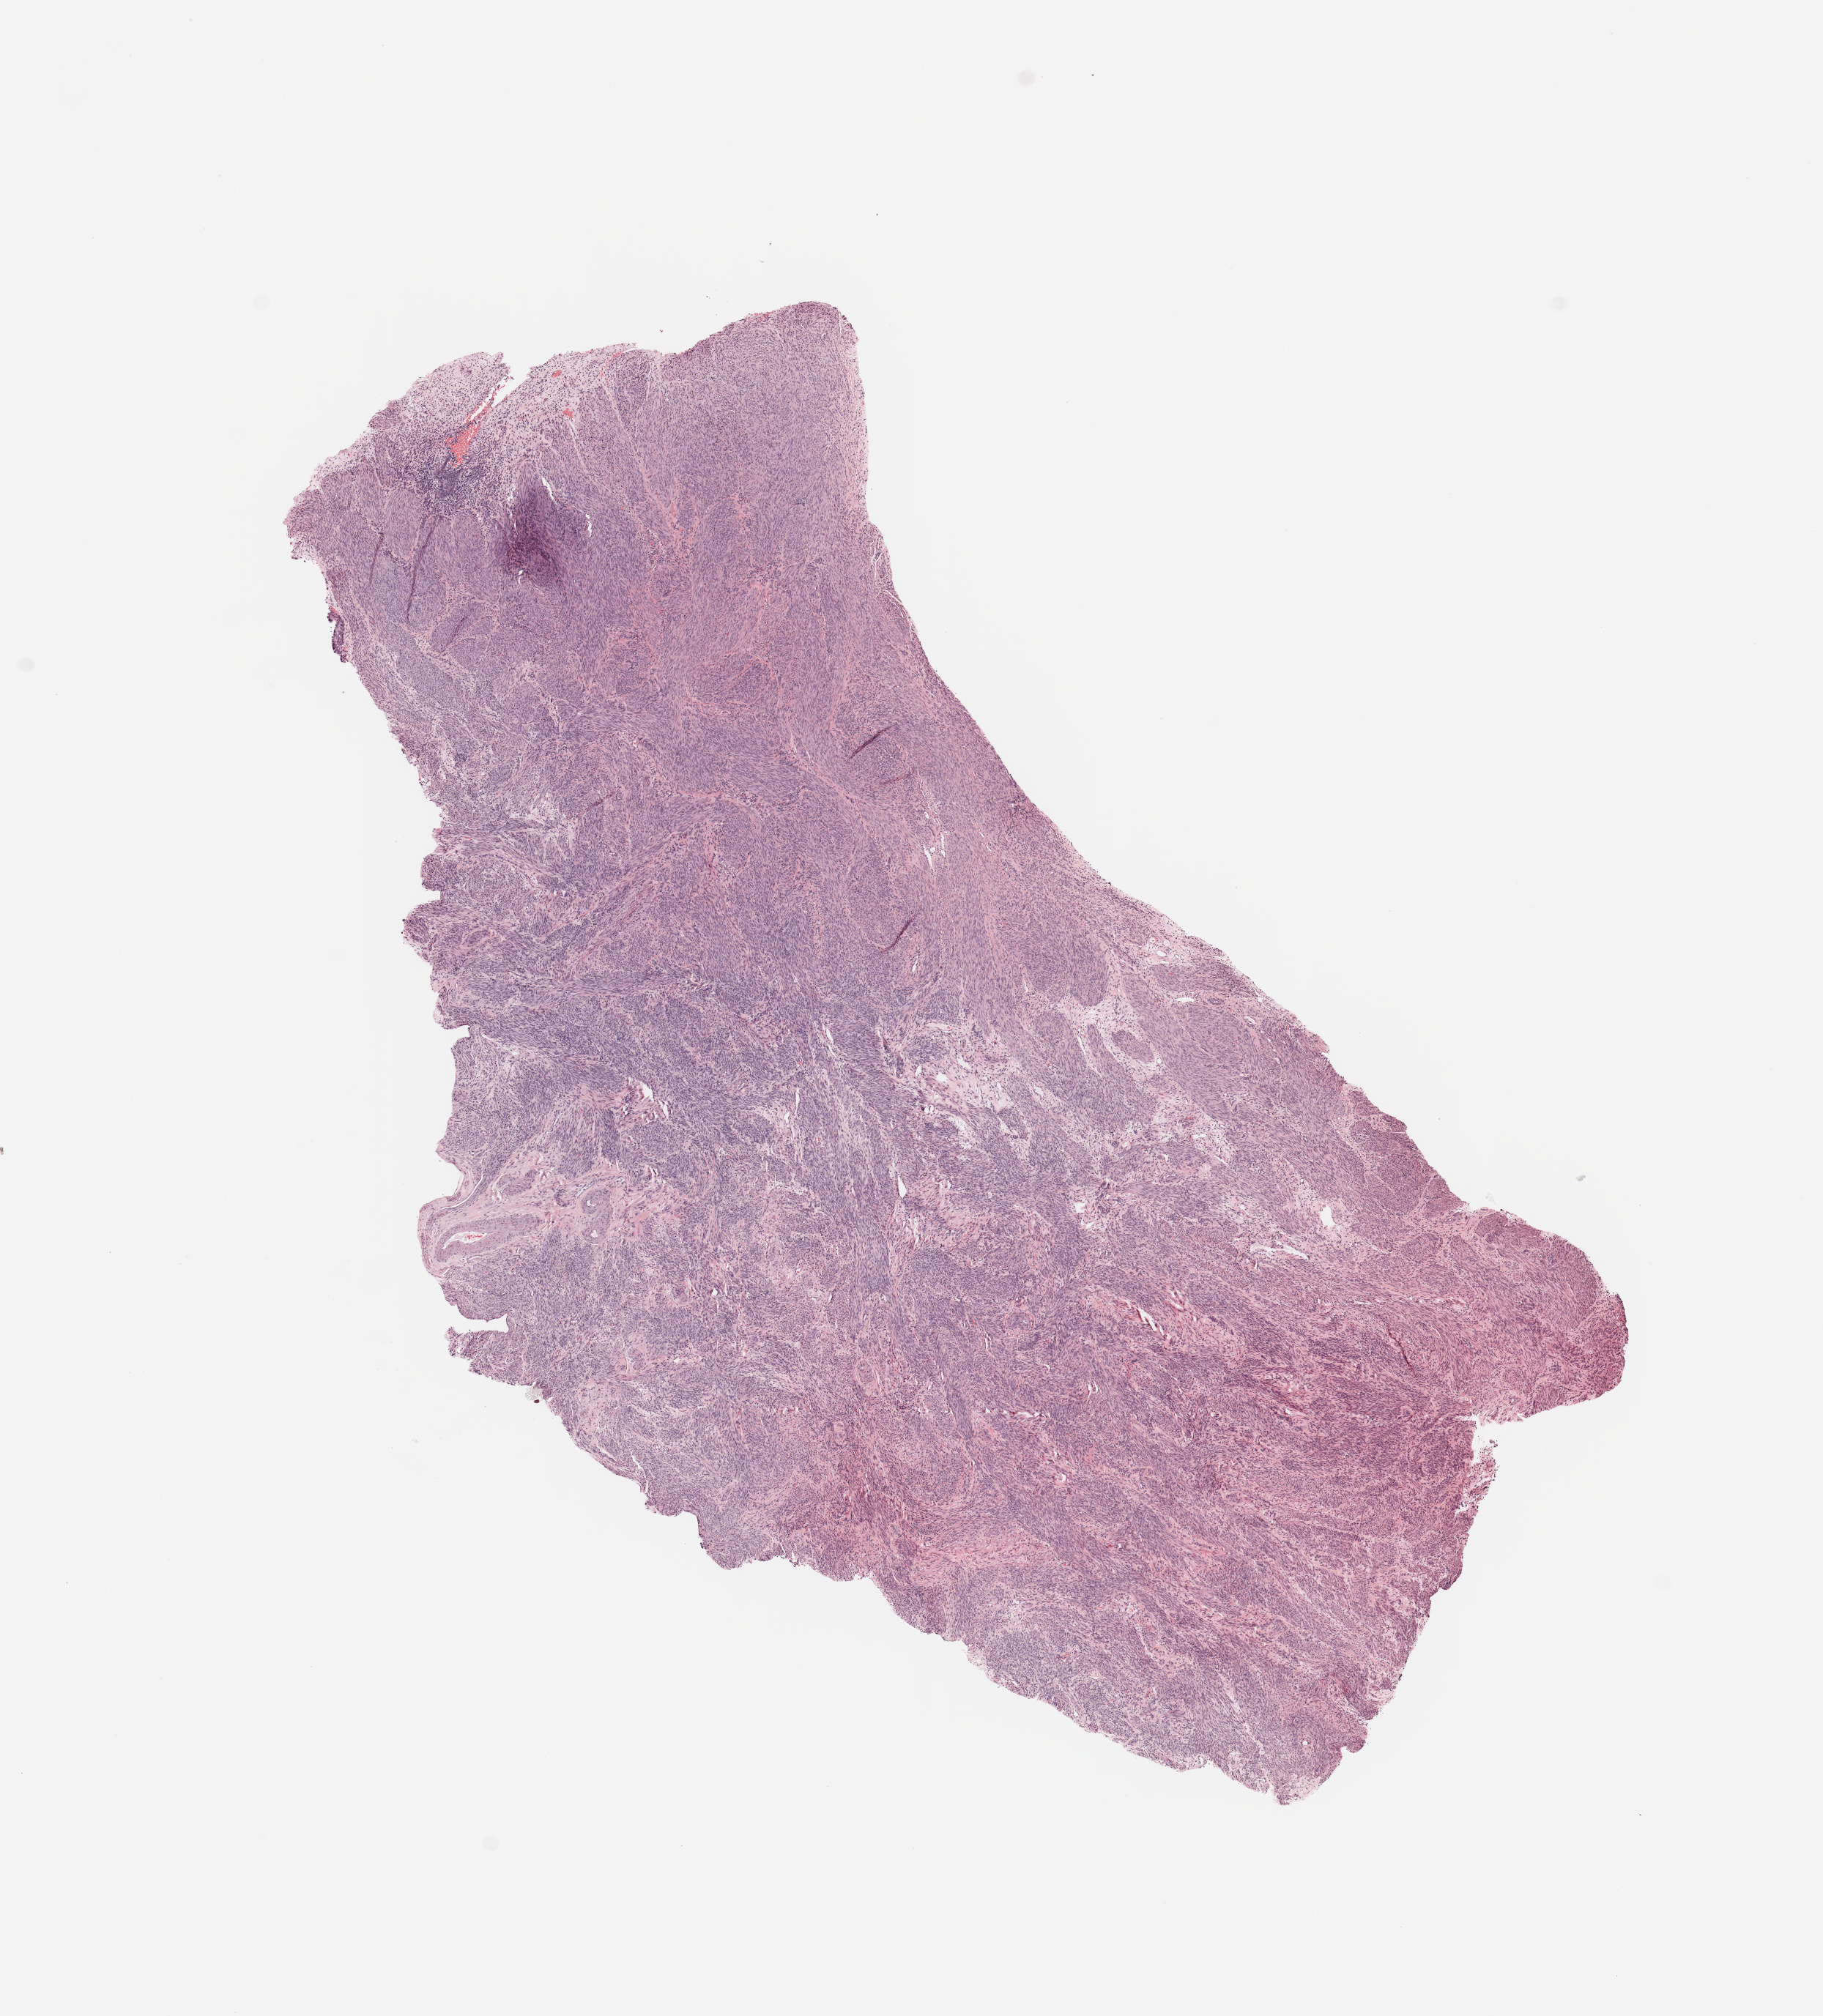
Digitized Hematoxylin and eosin (H&E) stained tissue section (whole slide) — a low-resolution overview of the entire scanned area, about 9.8 x 10.9 mm, normal (non-tumour) tissue sample, uterus. Female, 77 y/o.
• this section: normal (non-tumour) tissue from the same patient
• patient diagnosis: Endometrioid adenocarcinoma, NOS